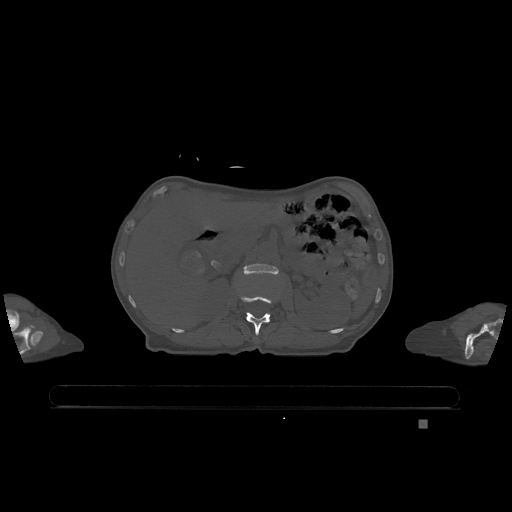
CT including the spine, one axial slice. Slice 461 of 1317 in the series (ordered by position). Bone window (W 1800 / L 400 HU). 0.5 mm slice thickness. 512 × 512 image matrix. Patient: female, 74 years. From the clinical record (not read from this slice): primary cancer: lung; vertebrae with lytic lesions (as recorded): T1, T4, T5, T6, L4, L5.
Structures marked on this image (semi-automatic segmentation, software-assisted and operator-edited):
- L1 vertebra: bounding box (x1, y1, x2, y2) in pixels: (240, 296, 273, 335)
- L2 vertebra: (244, 263, 278, 275)